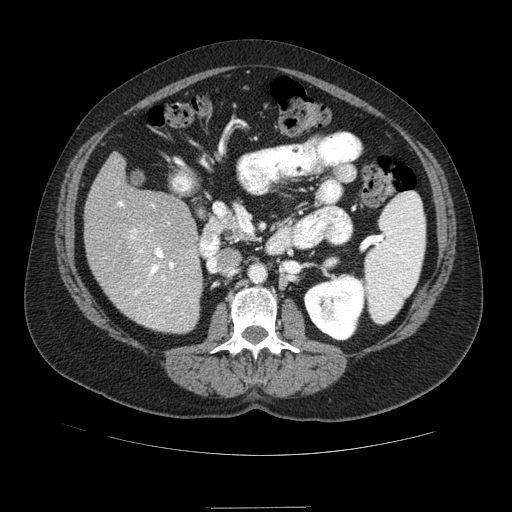
Contrast-enhanced abdominal CT (liver protocol), one axial slice. Slice 34 of 89 in the series (ordered by position). Reconstruction kernel STANDARD. Soft-tissue window (W 400 / L 40 HU). 2.5 mm slice thickness. 512 × 512 image matrix, field of view 400 × 400 mm. Case-level facts recorded for this patient, not image findings: diagnosis: hepatocellular carcinoma (patient treated with transarterial chemoembolisation; whether this scan precedes or follows treatment is not stated here); TNM stage (as recorded): Stage-IIIB; Child-Pugh class: A; tumour nodularity: multinodular.
Outlined on this slice (semi-automatically segmented with operator editing):
- liver parenchyma outside the tumour (the mass and vessels are separate outlines, so this box may not span the whole liver): box from (x=84, y=153) to (x=202, y=332) px
- liver vessels: (x=118, y=202)–(x=174, y=317)